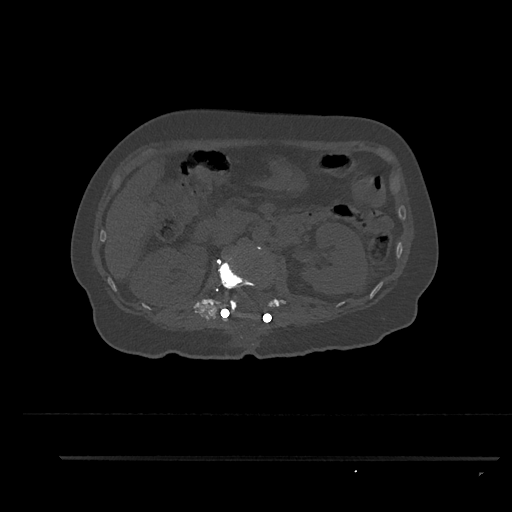
CT including the spine, one axial slice; slice 195 of 797 in the series (ordered by position); reconstruction kernel Br40s/3; 120 kVp; bone window (W 1800 / L 400 HU); 0.5 mm slice thickness; 512 × 512 image matrix, field of view 408 × 408 mm. Patient: female, 44 years. Case-level facts recorded for this patient, not image findings: primary cancer: renal.
Structures marked on this image (semi-automatic segmentation, software-assisted and operator-edited):
- L1 vertebra: bounding box <218,257,279,317> (left, top, right, bottom; pixels)
- L2 vertebra: <224,246,266,315>